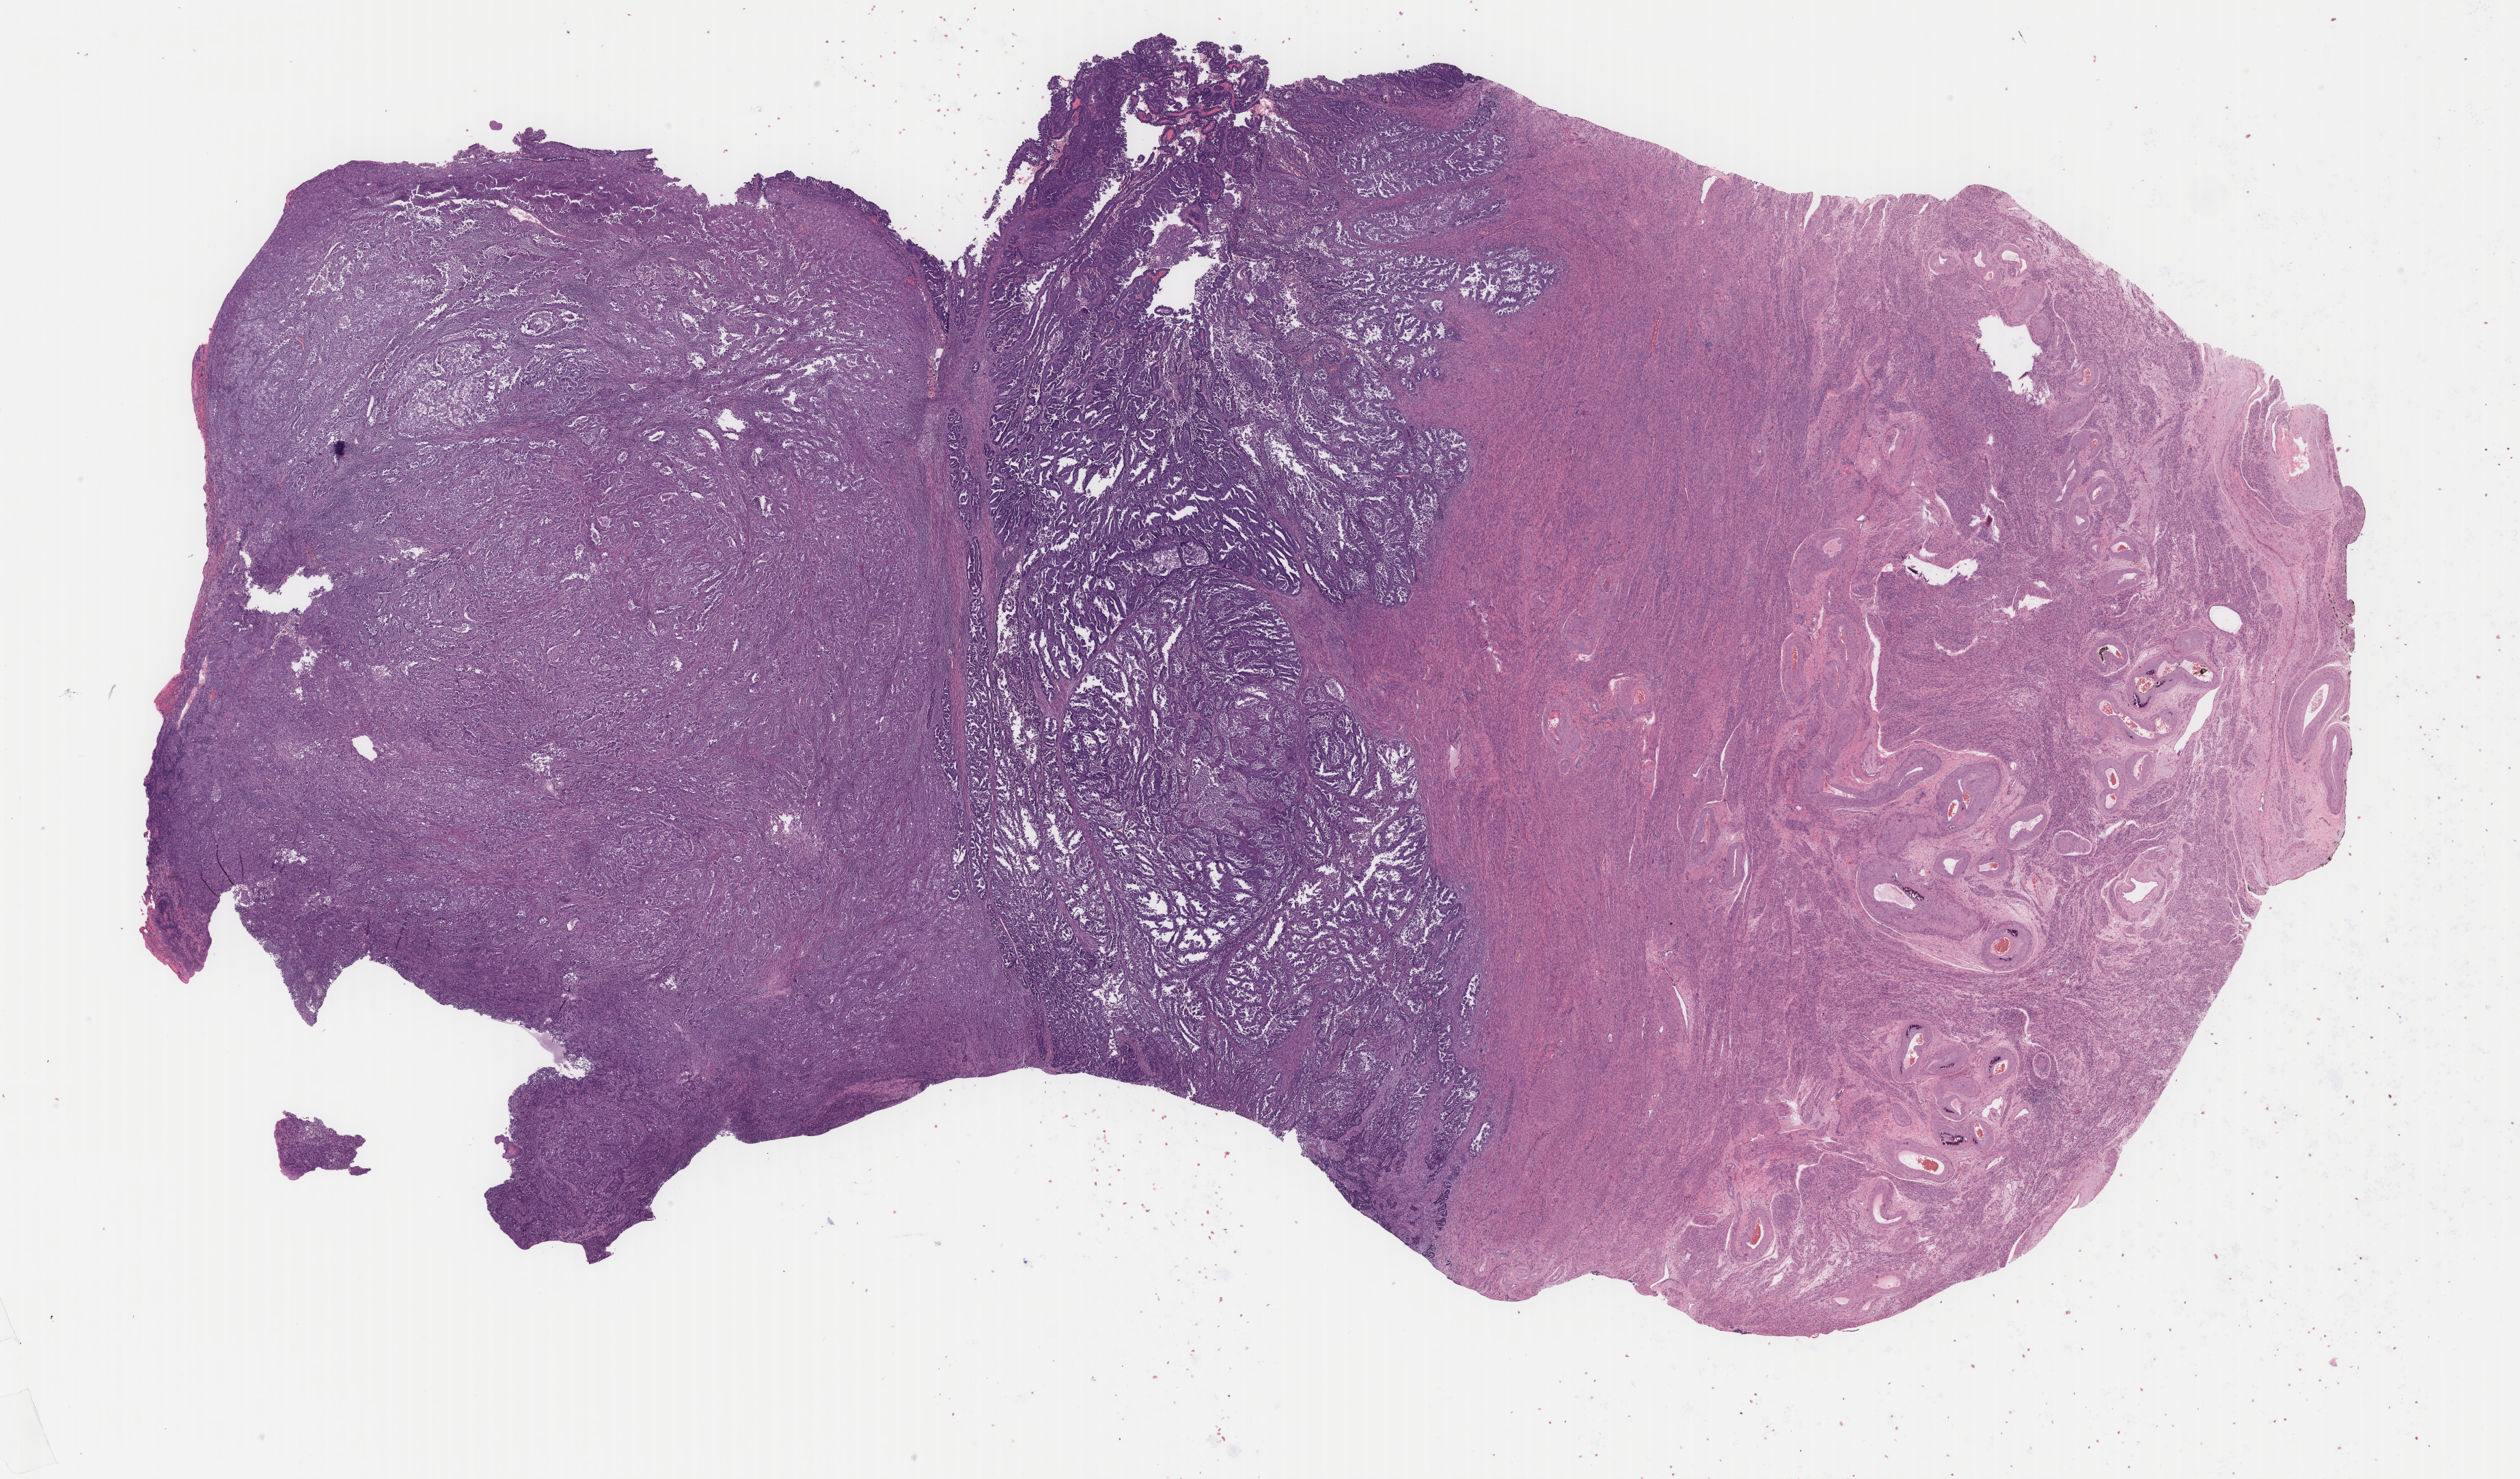
H&E whole-slide image — a low-resolution overview of the entire scanned area, about 29.3 x 17.2 mm (slide scanned at 40x); formalin-fixed paraffin-embedded (FFPE) diagnostic section; primary tumour sample from the uterus. Female patient; age at initial diagnosis 77 years. Histologic grade: G3 (poorly differentiated).
* FIGO stage: IIIC
* histologic diagnosis: Serous cystadenocarcinoma, NOS (endometrium)